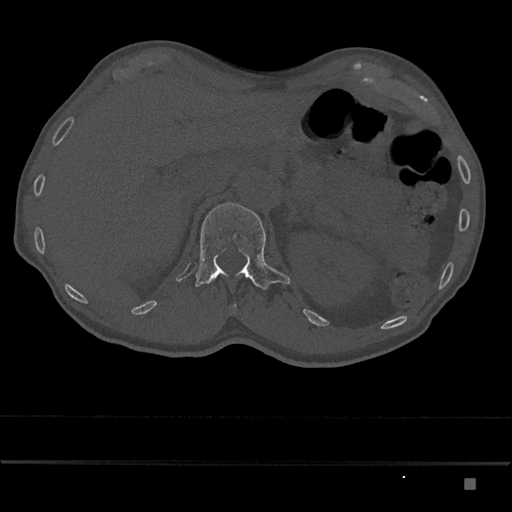
CT including the spine, one axial slice. Position 556 of 797 along the scan axis. Reconstruction kernel Br40s/3. Bone window (W 1800 / L 400 HU). 512 × 512 image matrix, field of view 390 × 390 mm. Male patient, age 72 years. Case-level facts recorded for this patient, not image findings: primary cancer: prostate.
Structures marked on this image (semi-automatically segmented with operator editing):
- L1 vertebra: bounding box <195,202,290,289> (left, top, right, bottom; pixels)
- T12 vertebra: <210,278,215,282>